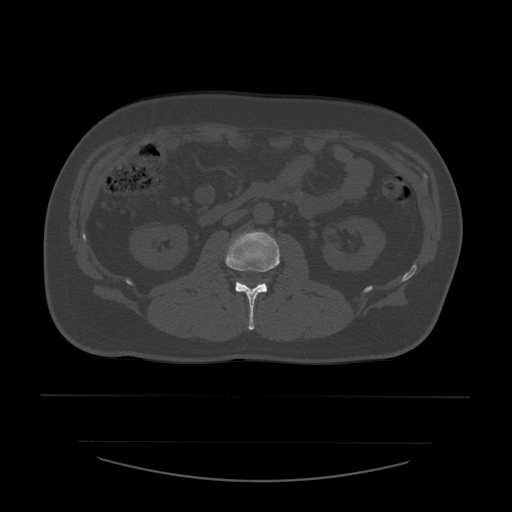
CT including the spine, one axial slice. Slice 194 of 532 in the series (ordered by position). Bone window (W 1800 / L 400 HU). 1.25 mm slice thickness. 512 × 512 image matrix. Patient age 44 years. Case-level facts recorded for this patient, not image findings: primary cancer: soft tissue sarcoma.
Annotated regions visible in this slice (semi-automatically segmented with operator editing):
- L2 vertebra: box from (x=225, y=231) to (x=280, y=331) px